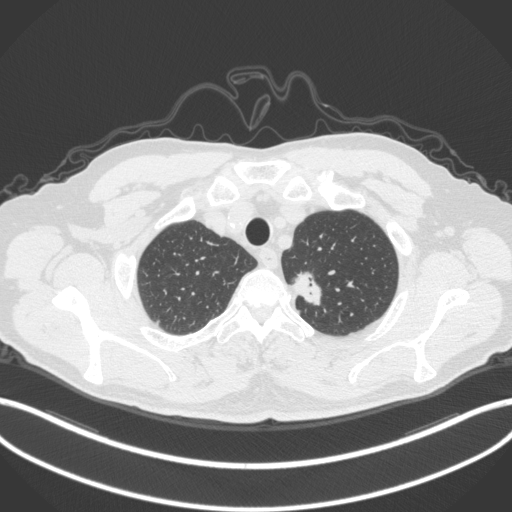
Chest CT, one axial slice; position 330 of 382 along the scan axis; reconstruction kernel B31f; lung window (W 1500 / L -600 HU); 1 mm slice thickness; 512 × 512 image matrix. Male patient, age 64 years. From the clinical record (not read from this slice): clinical TNM (as recorded): T1c N0 M0.
Structures marked on this image (rectangle marked by the reading radiologist):
- lung tumour (recorded histology: adenocarcinoma): bounding box (x1, y1, x2, y2) in pixels: (288, 265, 330, 311)